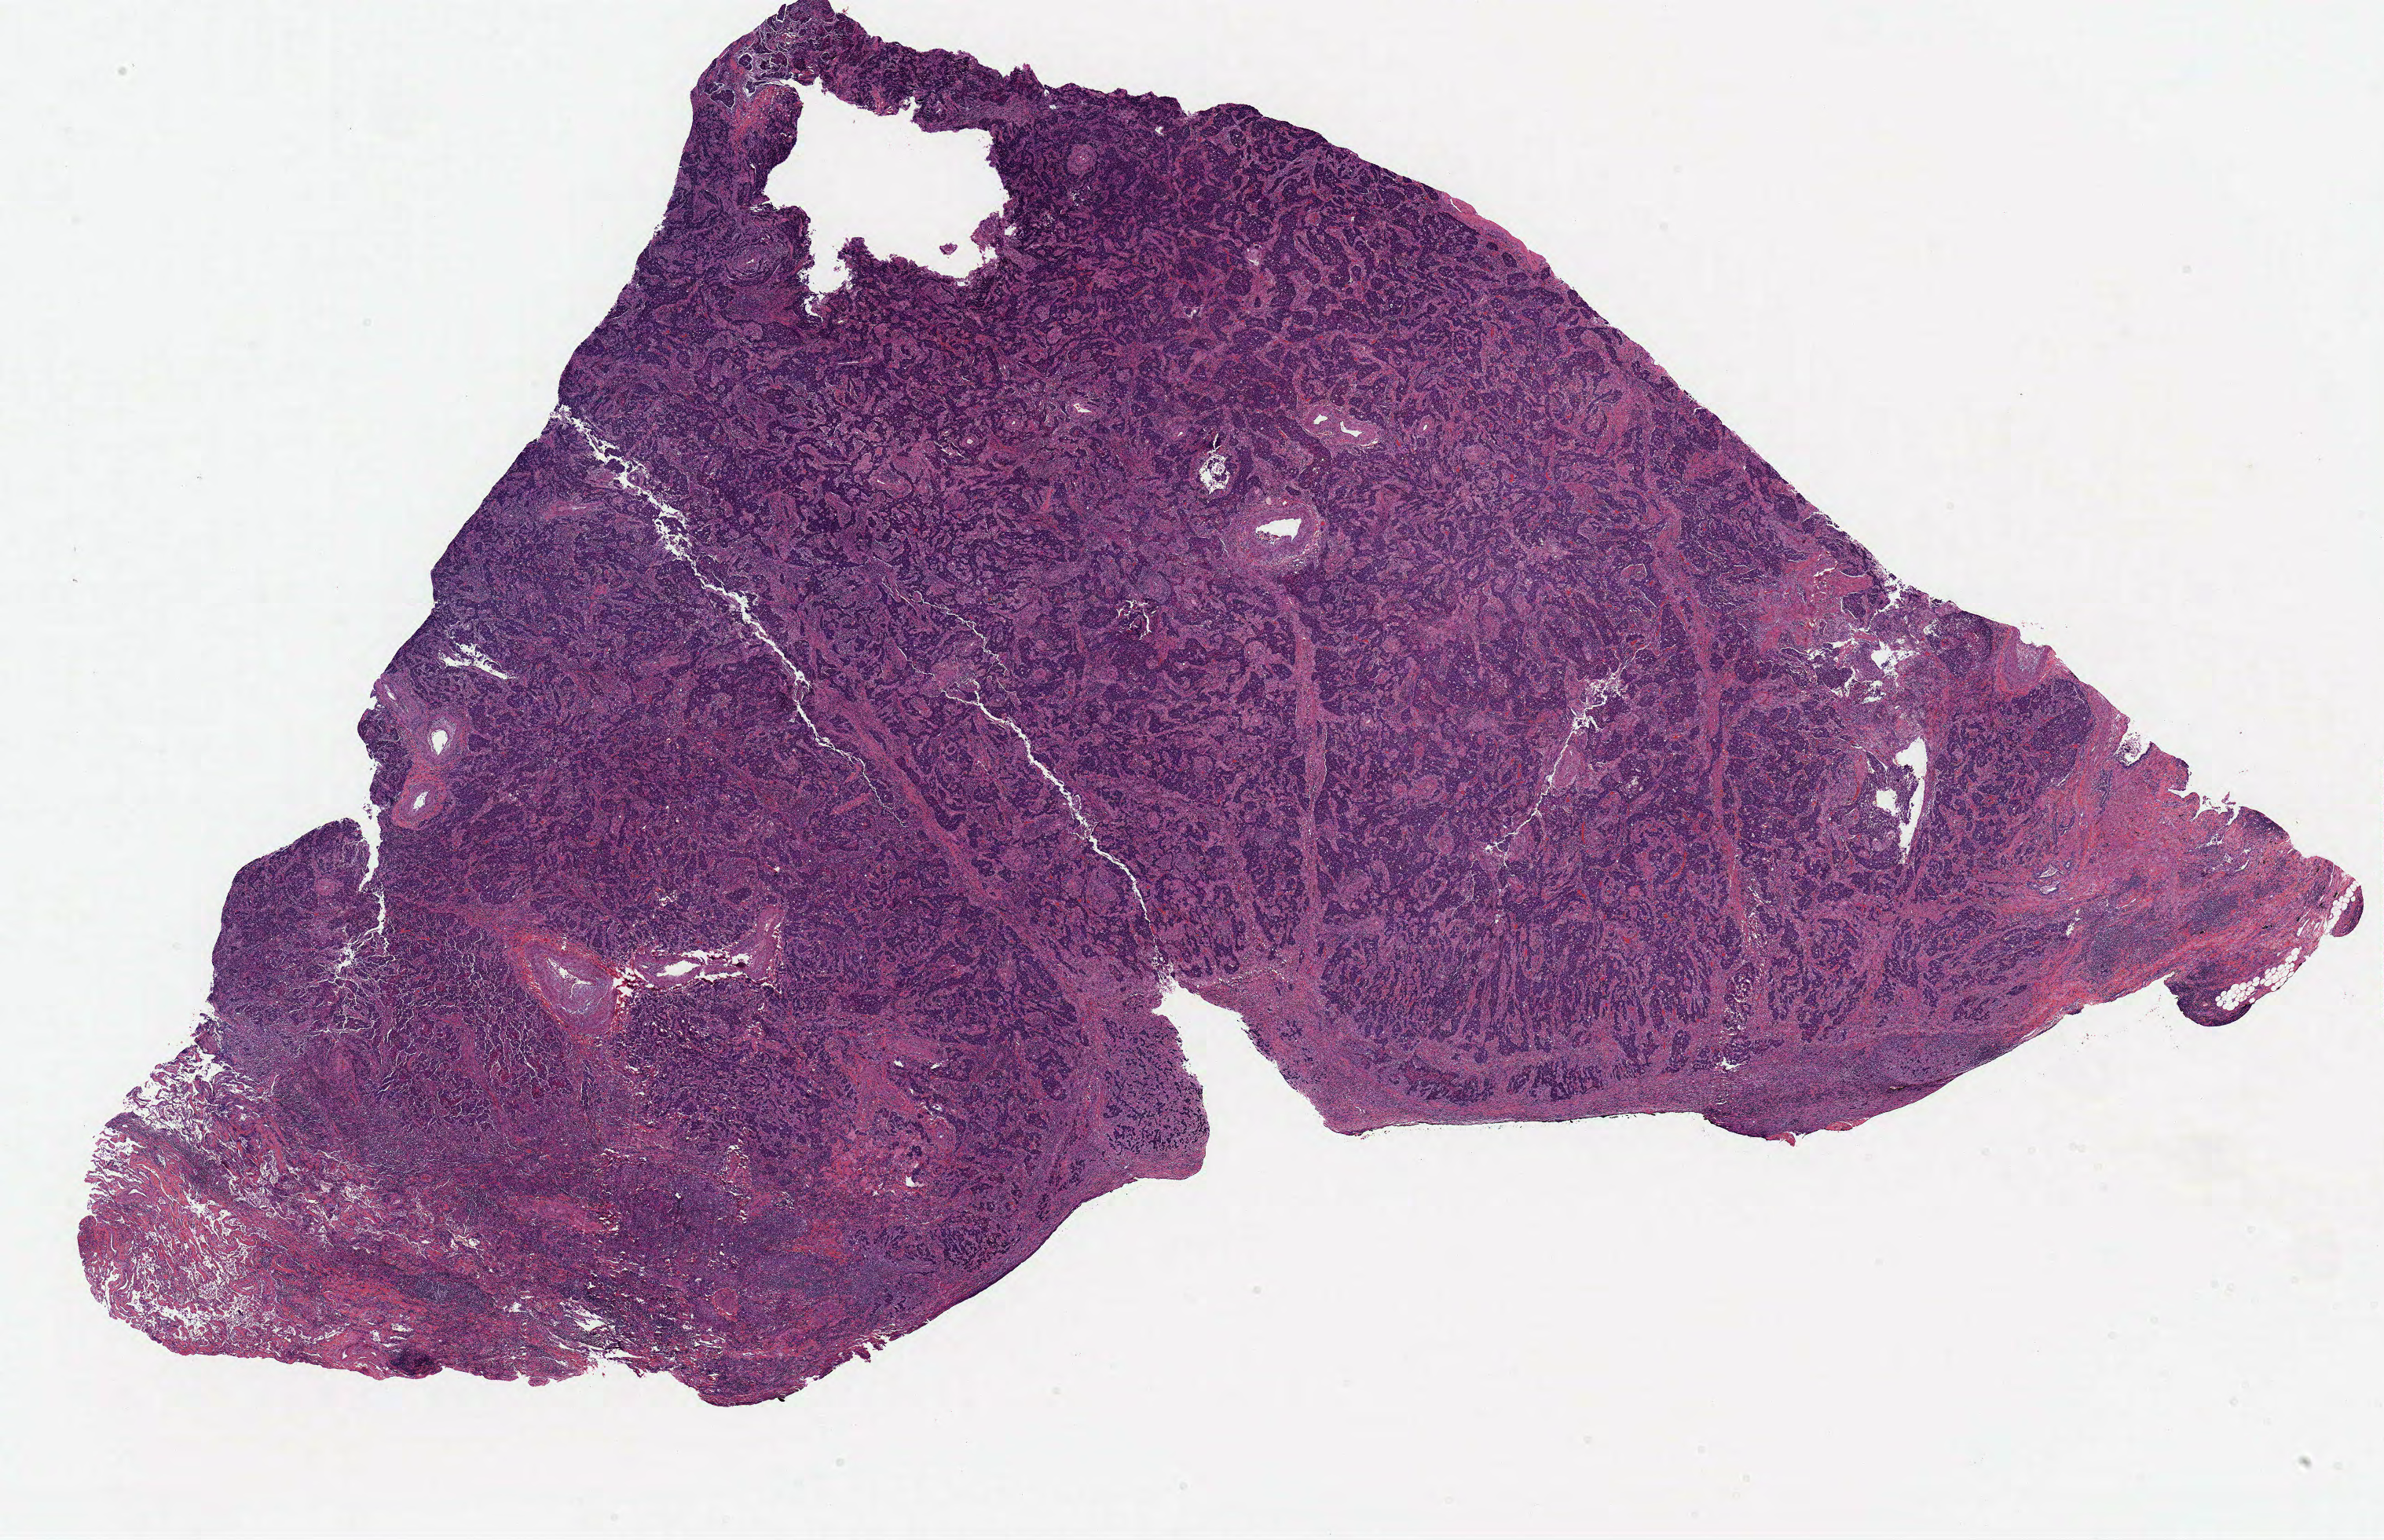
H&E-stained whole-slide image, whole scanned area (about 24.5 x 15.8 mm, from a 20x scan) shown as a low-resolution overview, FFPE section, lung, primary tumour sample. Patient: female, age at initial diagnosis 72 years.
AJCC pathologic stage: IA. Histologic diagnosis: Squamous cell carcinoma, NOS (lower lobe, lung). Laterality: right.